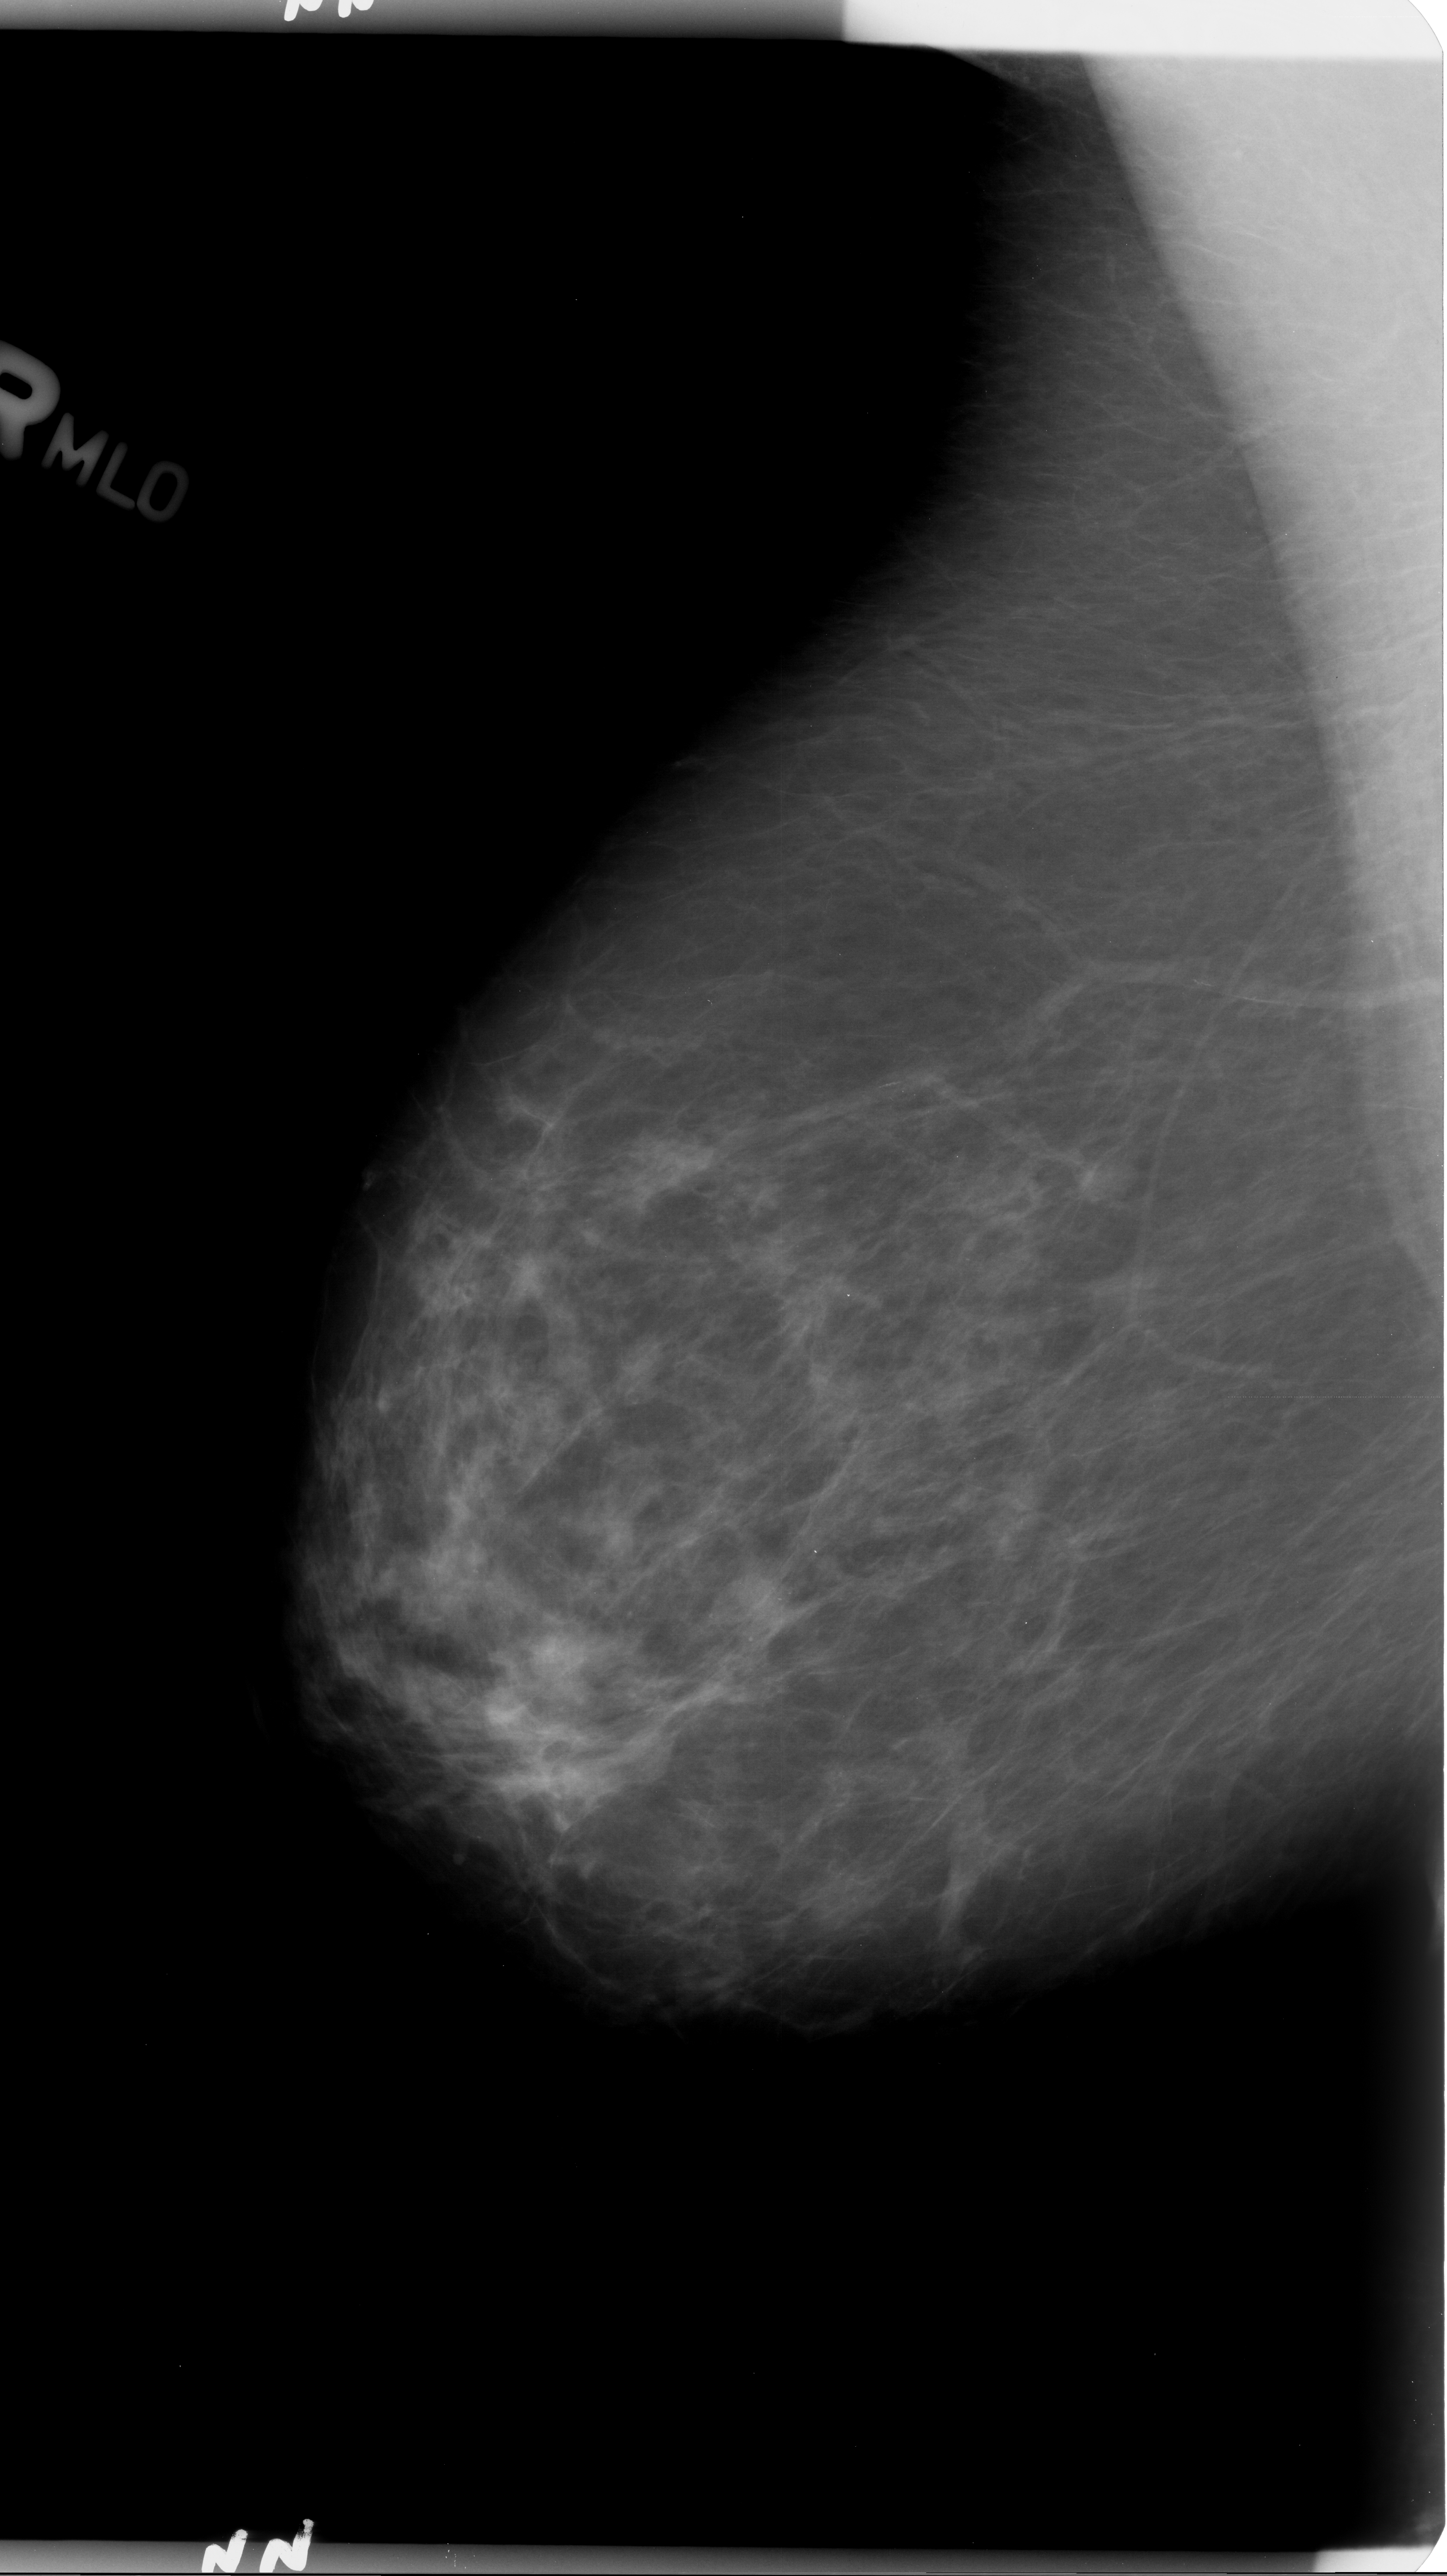
Scanned film-screen mammogram. Right breast. MLO view. Breast composition: scattered fibroglandular densities (BI-RADS density category 2 of 4). 1447 × 2576 image matrix.
Expert-marked regions of interest on this film, with their recorded descriptors:
- calcifications, morphology punctate / pleomorphic, distribution clustered; BI-RADS assessment category 3; subtlety rating 3 on a 1 (subtle) to 5 (obvious) scale; pathology (as recorded): benign: box from (x=706, y=1565) to (x=805, y=1668) px